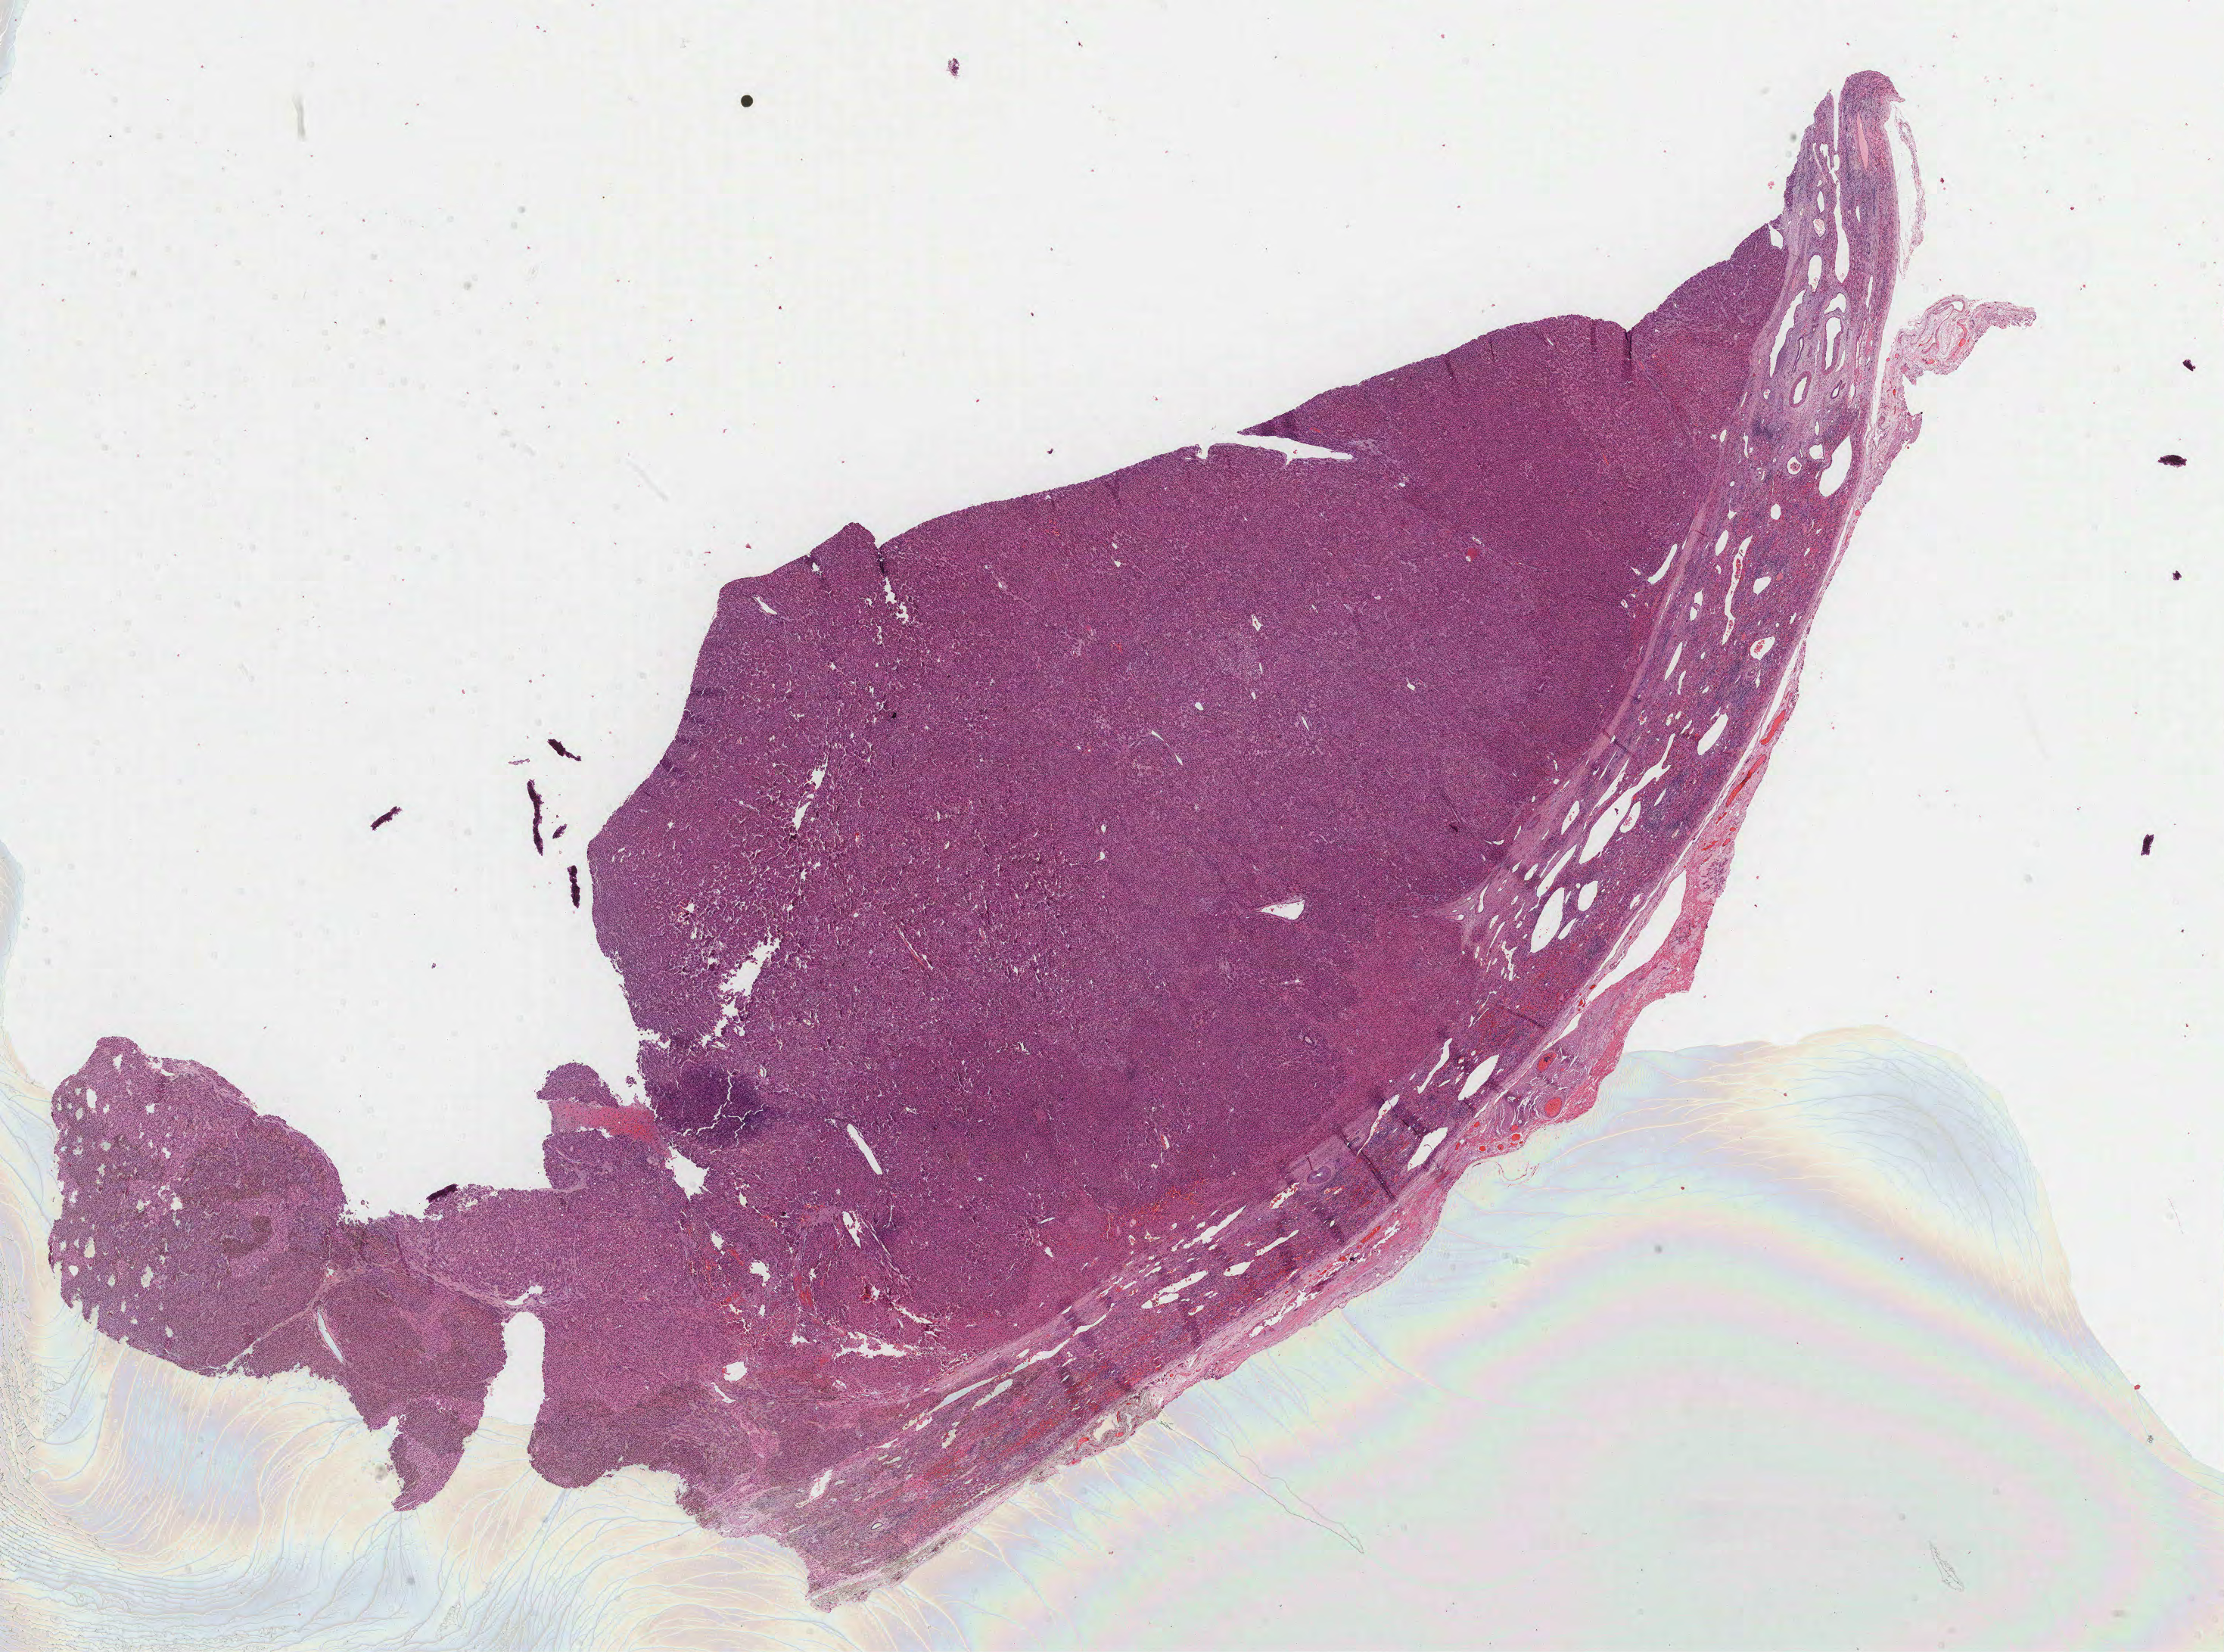
Whole-slide histology image, Hematoxylin and eosin (H&E) stained — shown as a low-resolution overview of the whole scanned area (about 23.7 x 17.6 mm, slide scanned at 40x). Formalin-fixed paraffin-embedded (FFPE) diagnostic section. Sample: primary tumour, liver. Female, age 82 years at initial diagnosis.
Histologic diagnosis: Hepatocellular carcinoma, NOS.